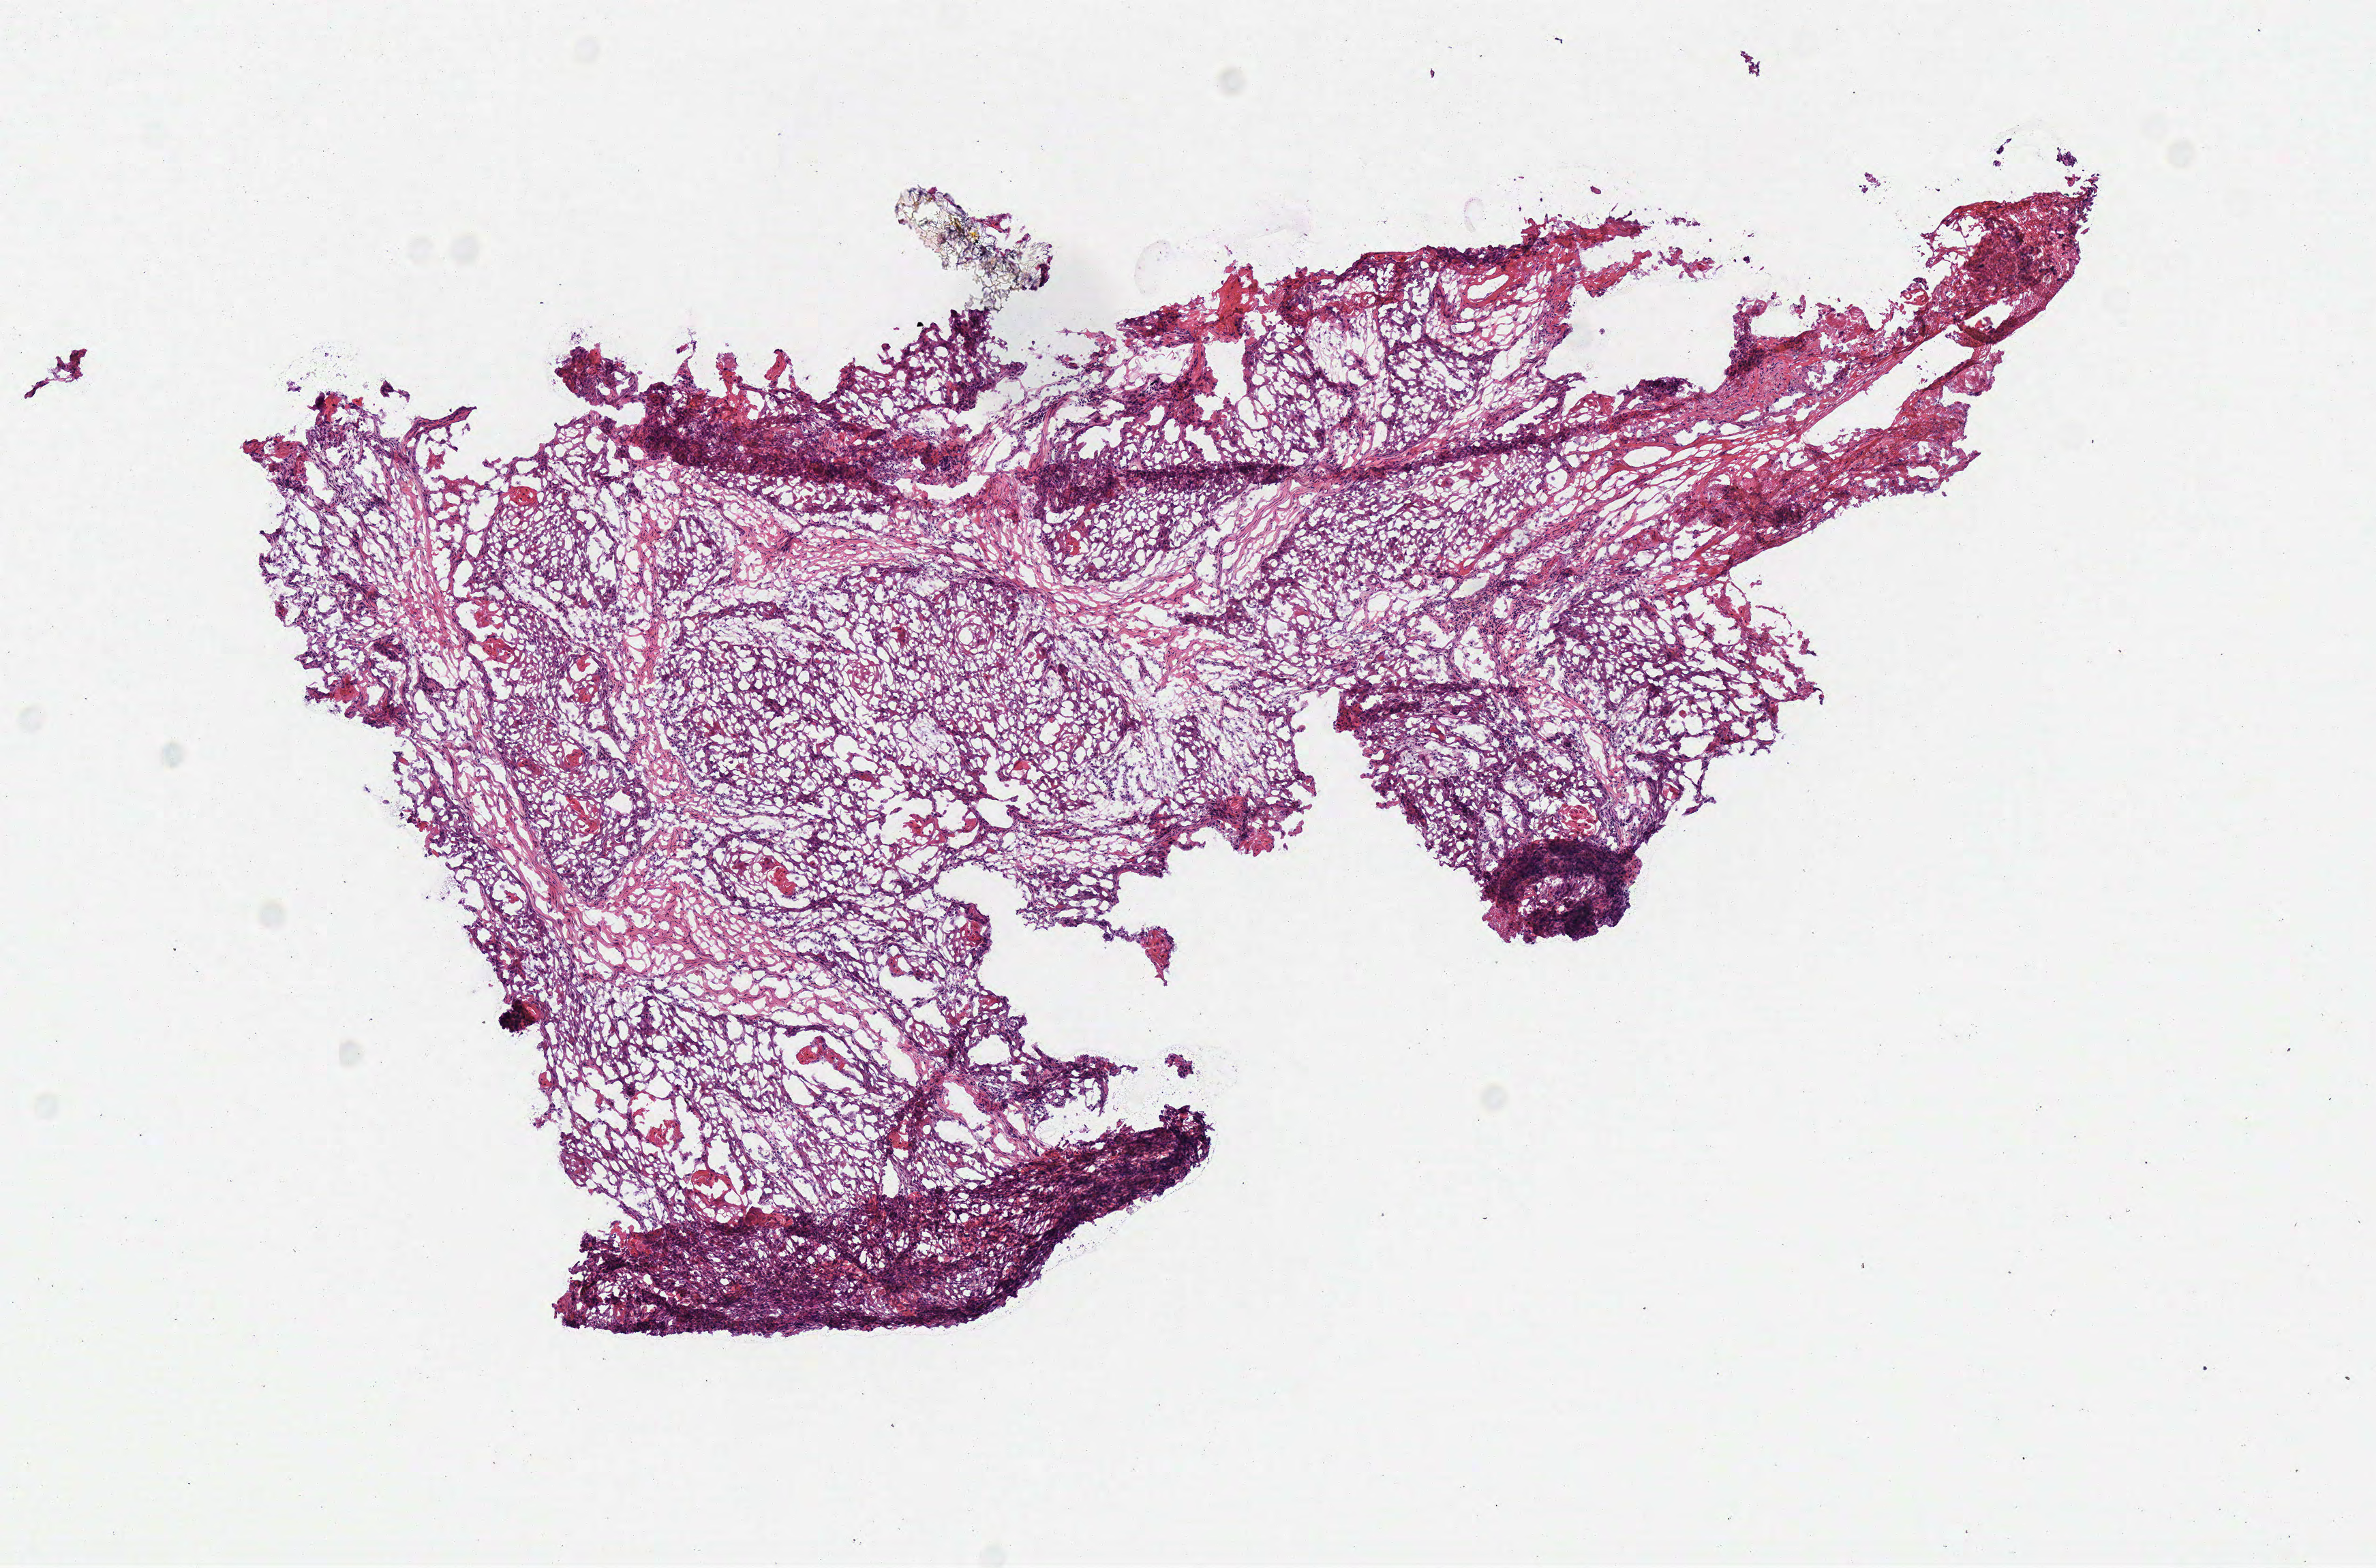
Digitized H&E-stained tissue section (whole slide), low-resolution overview of the scanned area, about 6.9 x 4.5 mm (acquisition: 40x scan); frozen section from the top of the tissue portion; sample: primary tumour, head and neck. Male, age 39 years at initial diagnosis. Histologic grade: G2 (moderately differentiated). Slide review estimates, as recorded: tumour cells 90%, tumour nuclei 70%, normal cells 0%, stromal cells 10%, necrosis 0%.
* diagnosis: Squamous cell carcinoma, NOS (overlapping lesion of lip, oral cavity and pharynx)
* AJCC pathologic stage: II